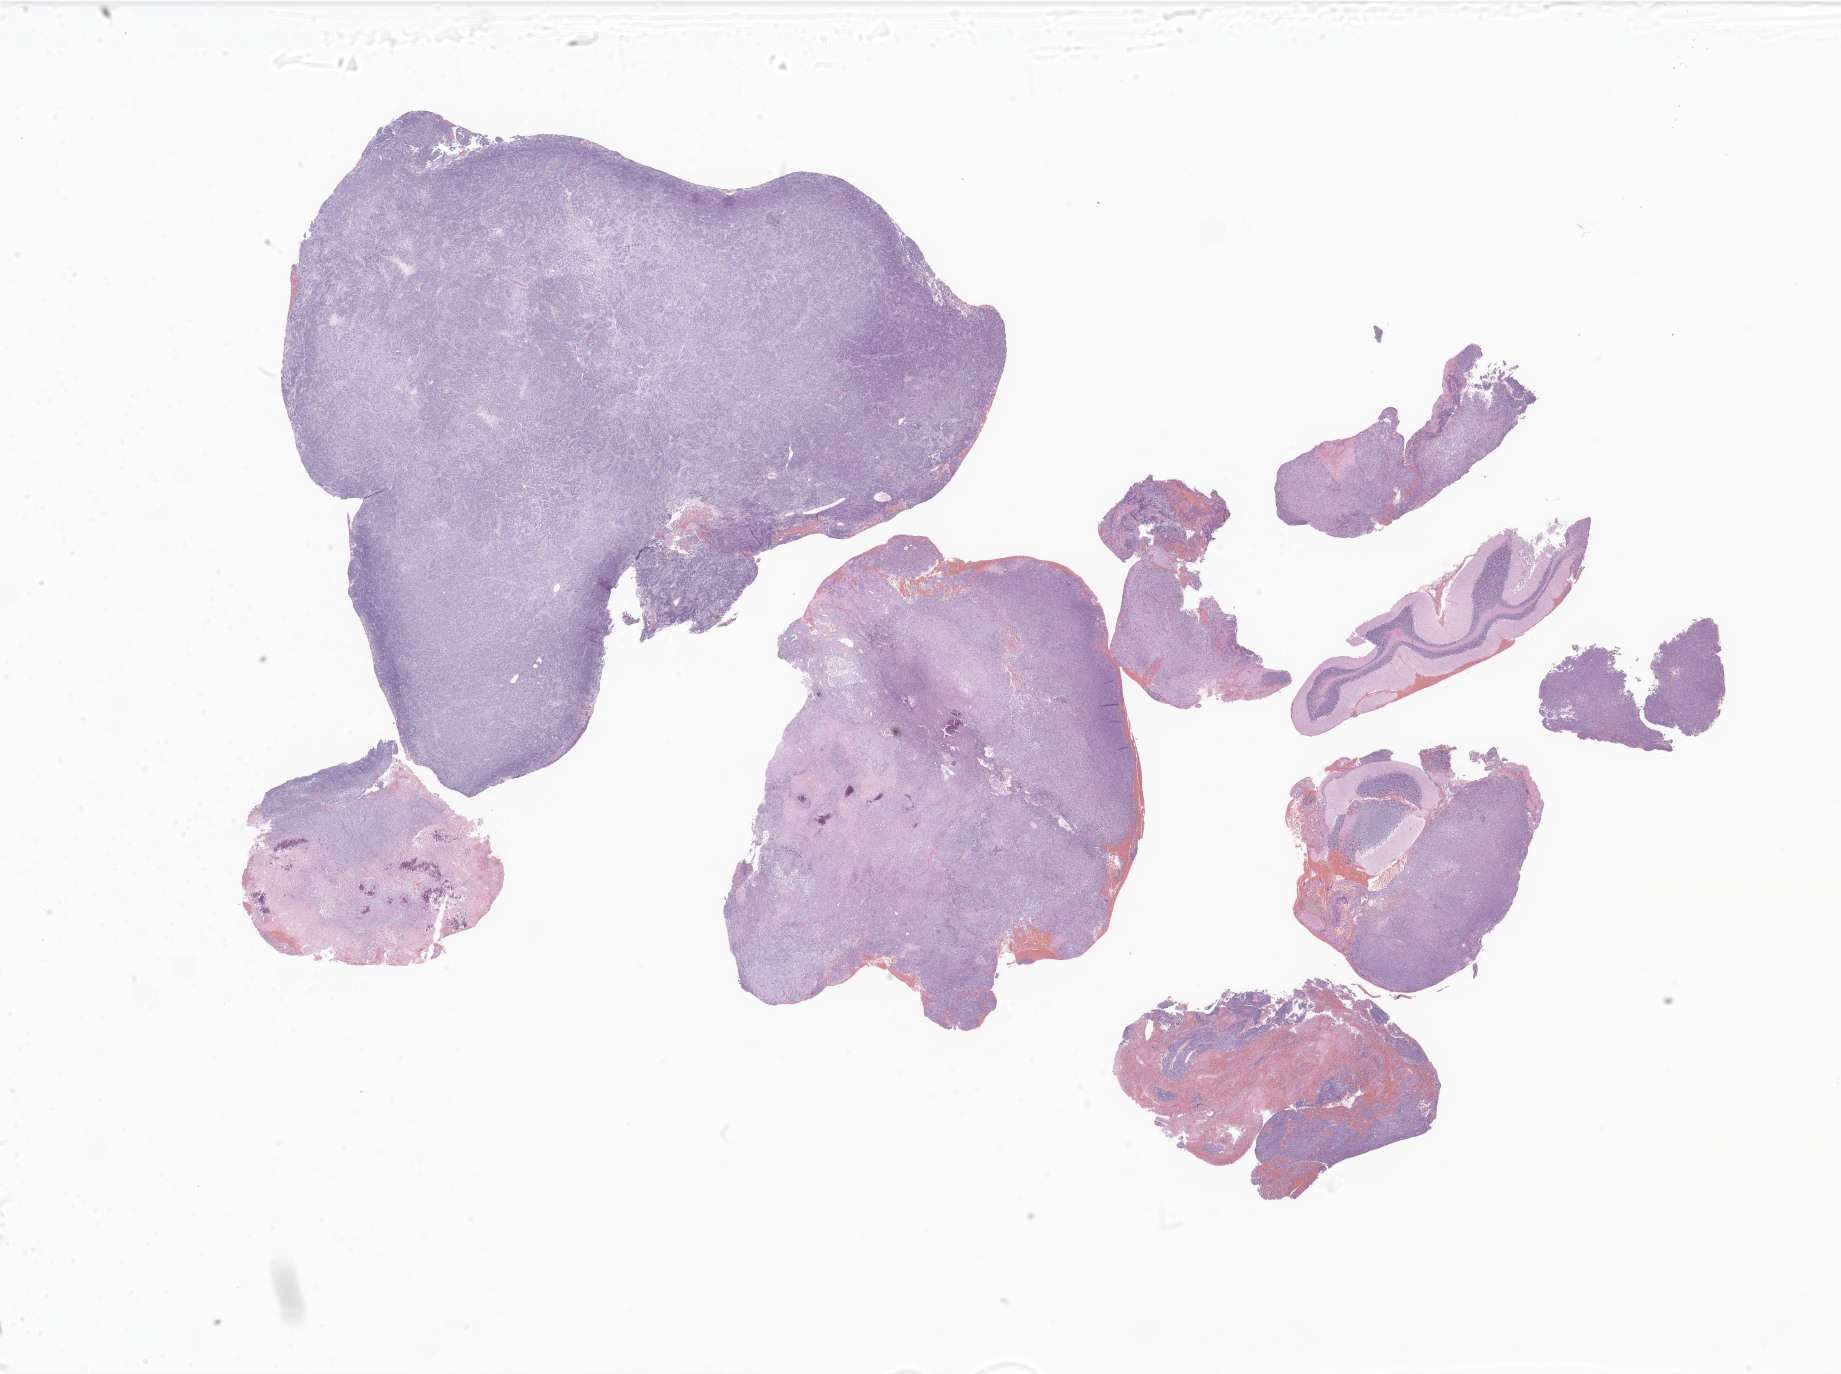
Hematoxylin and eosin (H&E) whole-slide image of tumor tissue from the brain, whole scanned area (about 31.1 x 23.2 mm) shown as a low-resolution overview, FFPE section. Patient female; age 762 days (about 2.1 years).
Diagnosis: Atypical teratoid/rhabdoid tumor.